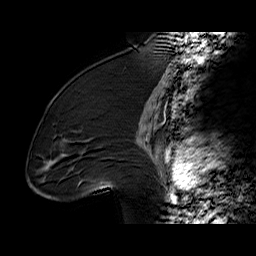
Breast MRI (dynamic contrast-enhanced), one sagittal slice. Slice 36 of 60 in the series (ordered by position). Dynamic contrast-enhanced series, time point 2 of 6 at this slice position (early post-contrast). 1.5 T. TE 6.2 ms, TR 32.4 ms. 4 mm slice thickness. 256 × 256 image matrix, field of view 200 × 200 mm. Female patient. From the clinical record (not read from this slice): setting: breast cancer imaged before/during neoadjuvant chemotherapy; receptor status: triple-negative.
Structures marked on this image (semi-automatic segmentation, software-assisted and operator-edited):
- analysis volume of interest (the breast-tissue region the enhancement analysis was run in; not a lesion): box from (x=36, y=97) to (x=134, y=196) px
- tumour enhancement mask (voxels above the 100 % enhancement threshold inside the analysis volume of interest): (x=62, y=140)–(x=105, y=184)